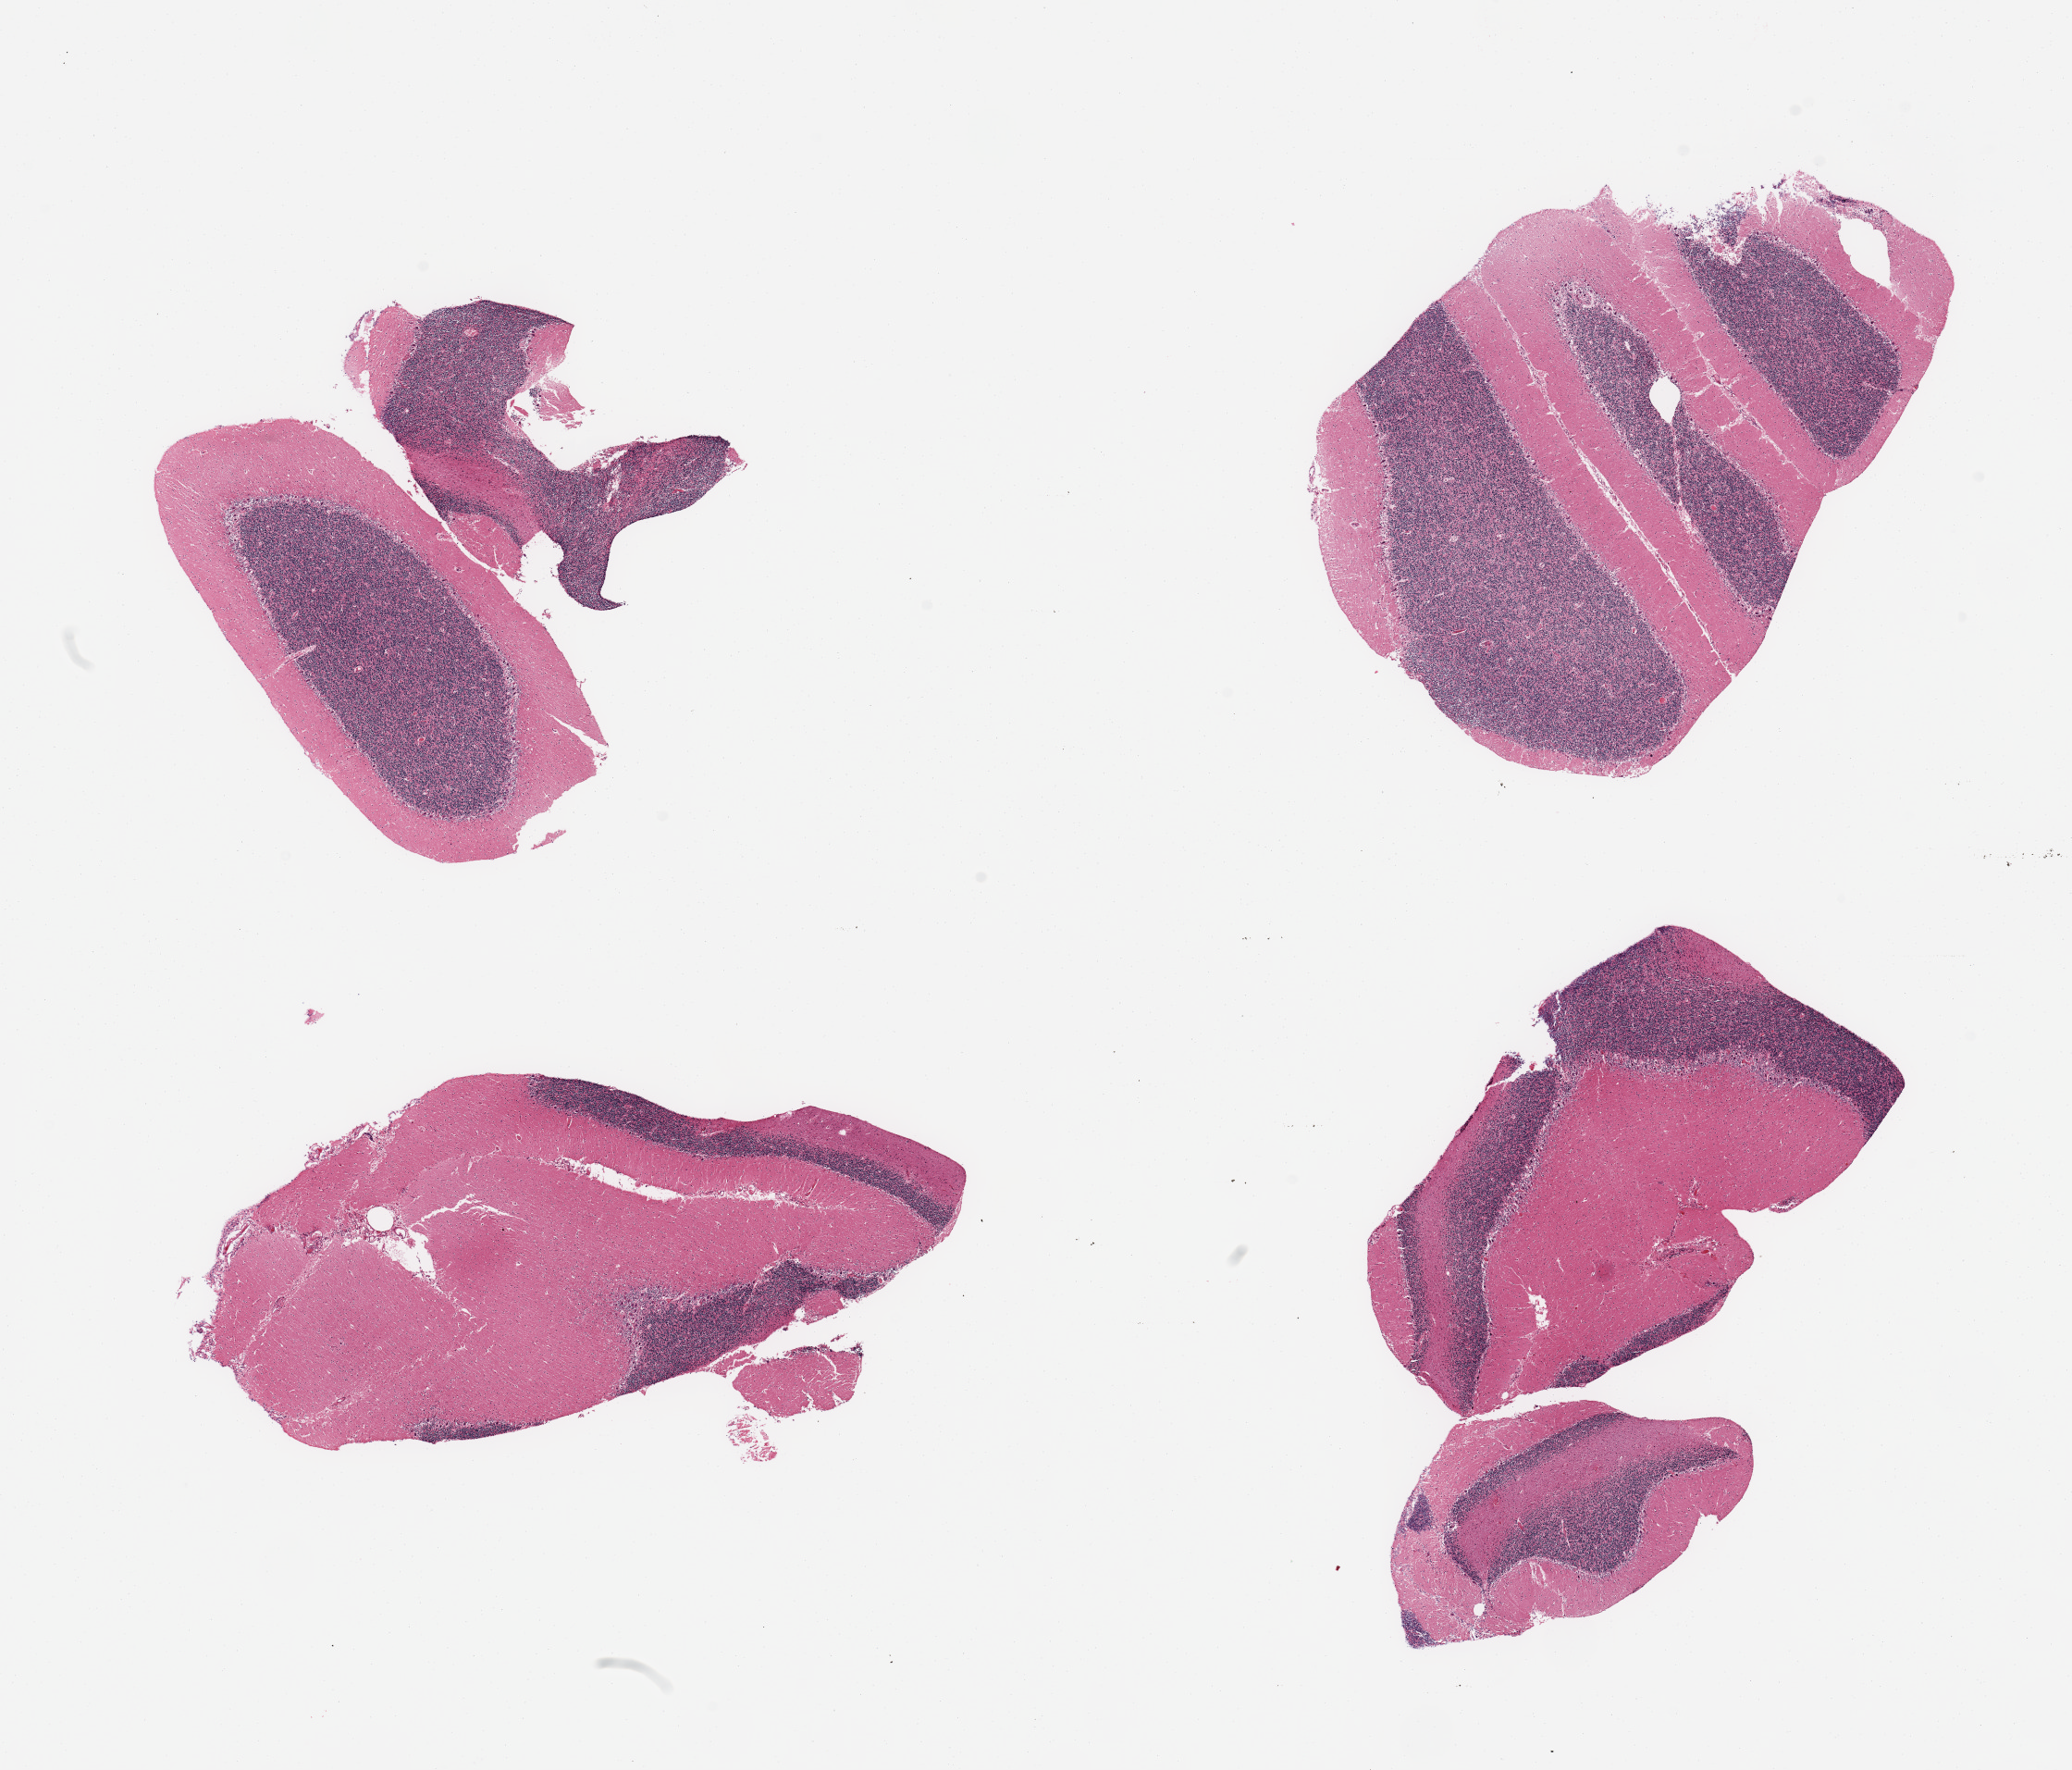
Digitized haematoxylin and eosin-stained section — a low-resolution overview of the entire scanned area, about 17.7 x 15.1 mm, PAXgene-fixed, paraffin-embedded tissue, target tissue: cerebellum, tissue donor sample. Donor sex: female.
Review note (as recorded): 4 pieces.